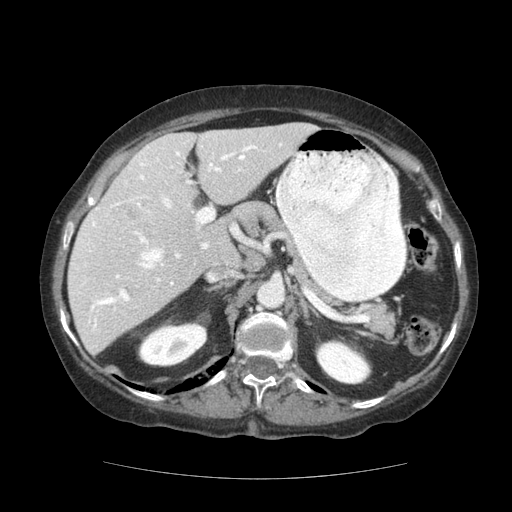
Contrast-enhanced abdominal CT (liver protocol), one axial slice; position 74 of 111 along the scan axis; 140 kVp; soft-tissue window (W 400 / L 40 HU); 2.5 mm slice thickness; 512 × 512 image matrix, field of view 360 × 360 mm. Case-level facts recorded for this patient, not image findings: diagnosis: hepatocellular carcinoma (patient treated with transarterial chemoembolisation; whether this scan precedes or follows treatment is not stated here); TNM stage (as recorded): Stage-I; Child-Pugh class: A; tumour nodularity: uninodular; tumour size: 7.3 cm.
Structures marked on this image (semi-automatic segmentation, software-assisted and operator-edited):
- liver parenchyma outside the tumour (the mass and vessels are separate outlines, so this box may not span the whole liver): bounding box <68,122,316,354> (left, top, right, bottom; pixels)
- liver vessels: <83,144,282,330>